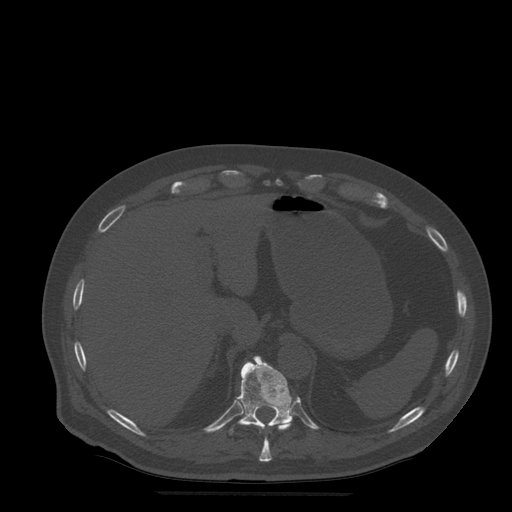
CT including the spine, one axial slice; position 253 of 522 along the scan axis; bone window (W 1800 / L 400 HU); 1.25 mm slice thickness; 512 × 512 image matrix, field of view 420 × 420 mm. Patient age 72 years. From the clinical record (not read from this slice): primary cancer: prostate.
Structures marked on this image (semi-automatically segmented with operator editing):
- T10 vertebra: bounding box <239,421,292,462> (left, top, right, bottom; pixels)
- T11 vertebra: <229,356,295,435>